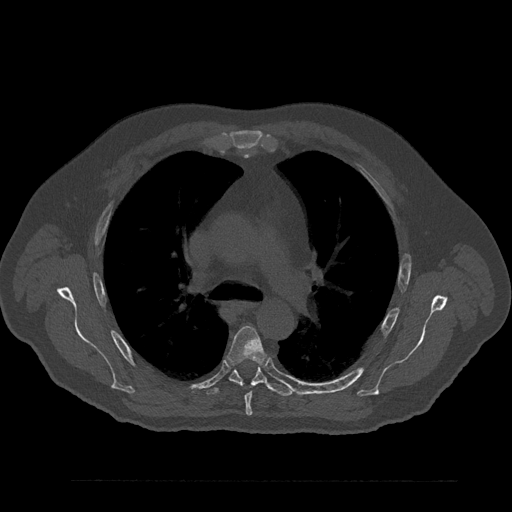
CT including the spine, one axial slice. Position 582 of 797 along the scan axis. Reconstruction kernel Br40s/3. 120 kVp. Bone window (W 1800 / L 400 HU). 0.5 mm slice thickness. 512 × 512 image matrix. Patient: male, 61 years. From the clinical record (not read from this slice): primary cancer: prostate.
Structures marked on this image (semi-automatic segmentation, software-assisted and operator-edited):
- T5 vertebra: bounding box <228,326,266,416> (left, top, right, bottom; pixels)
- T6 vertebra: <206,363,293,397>